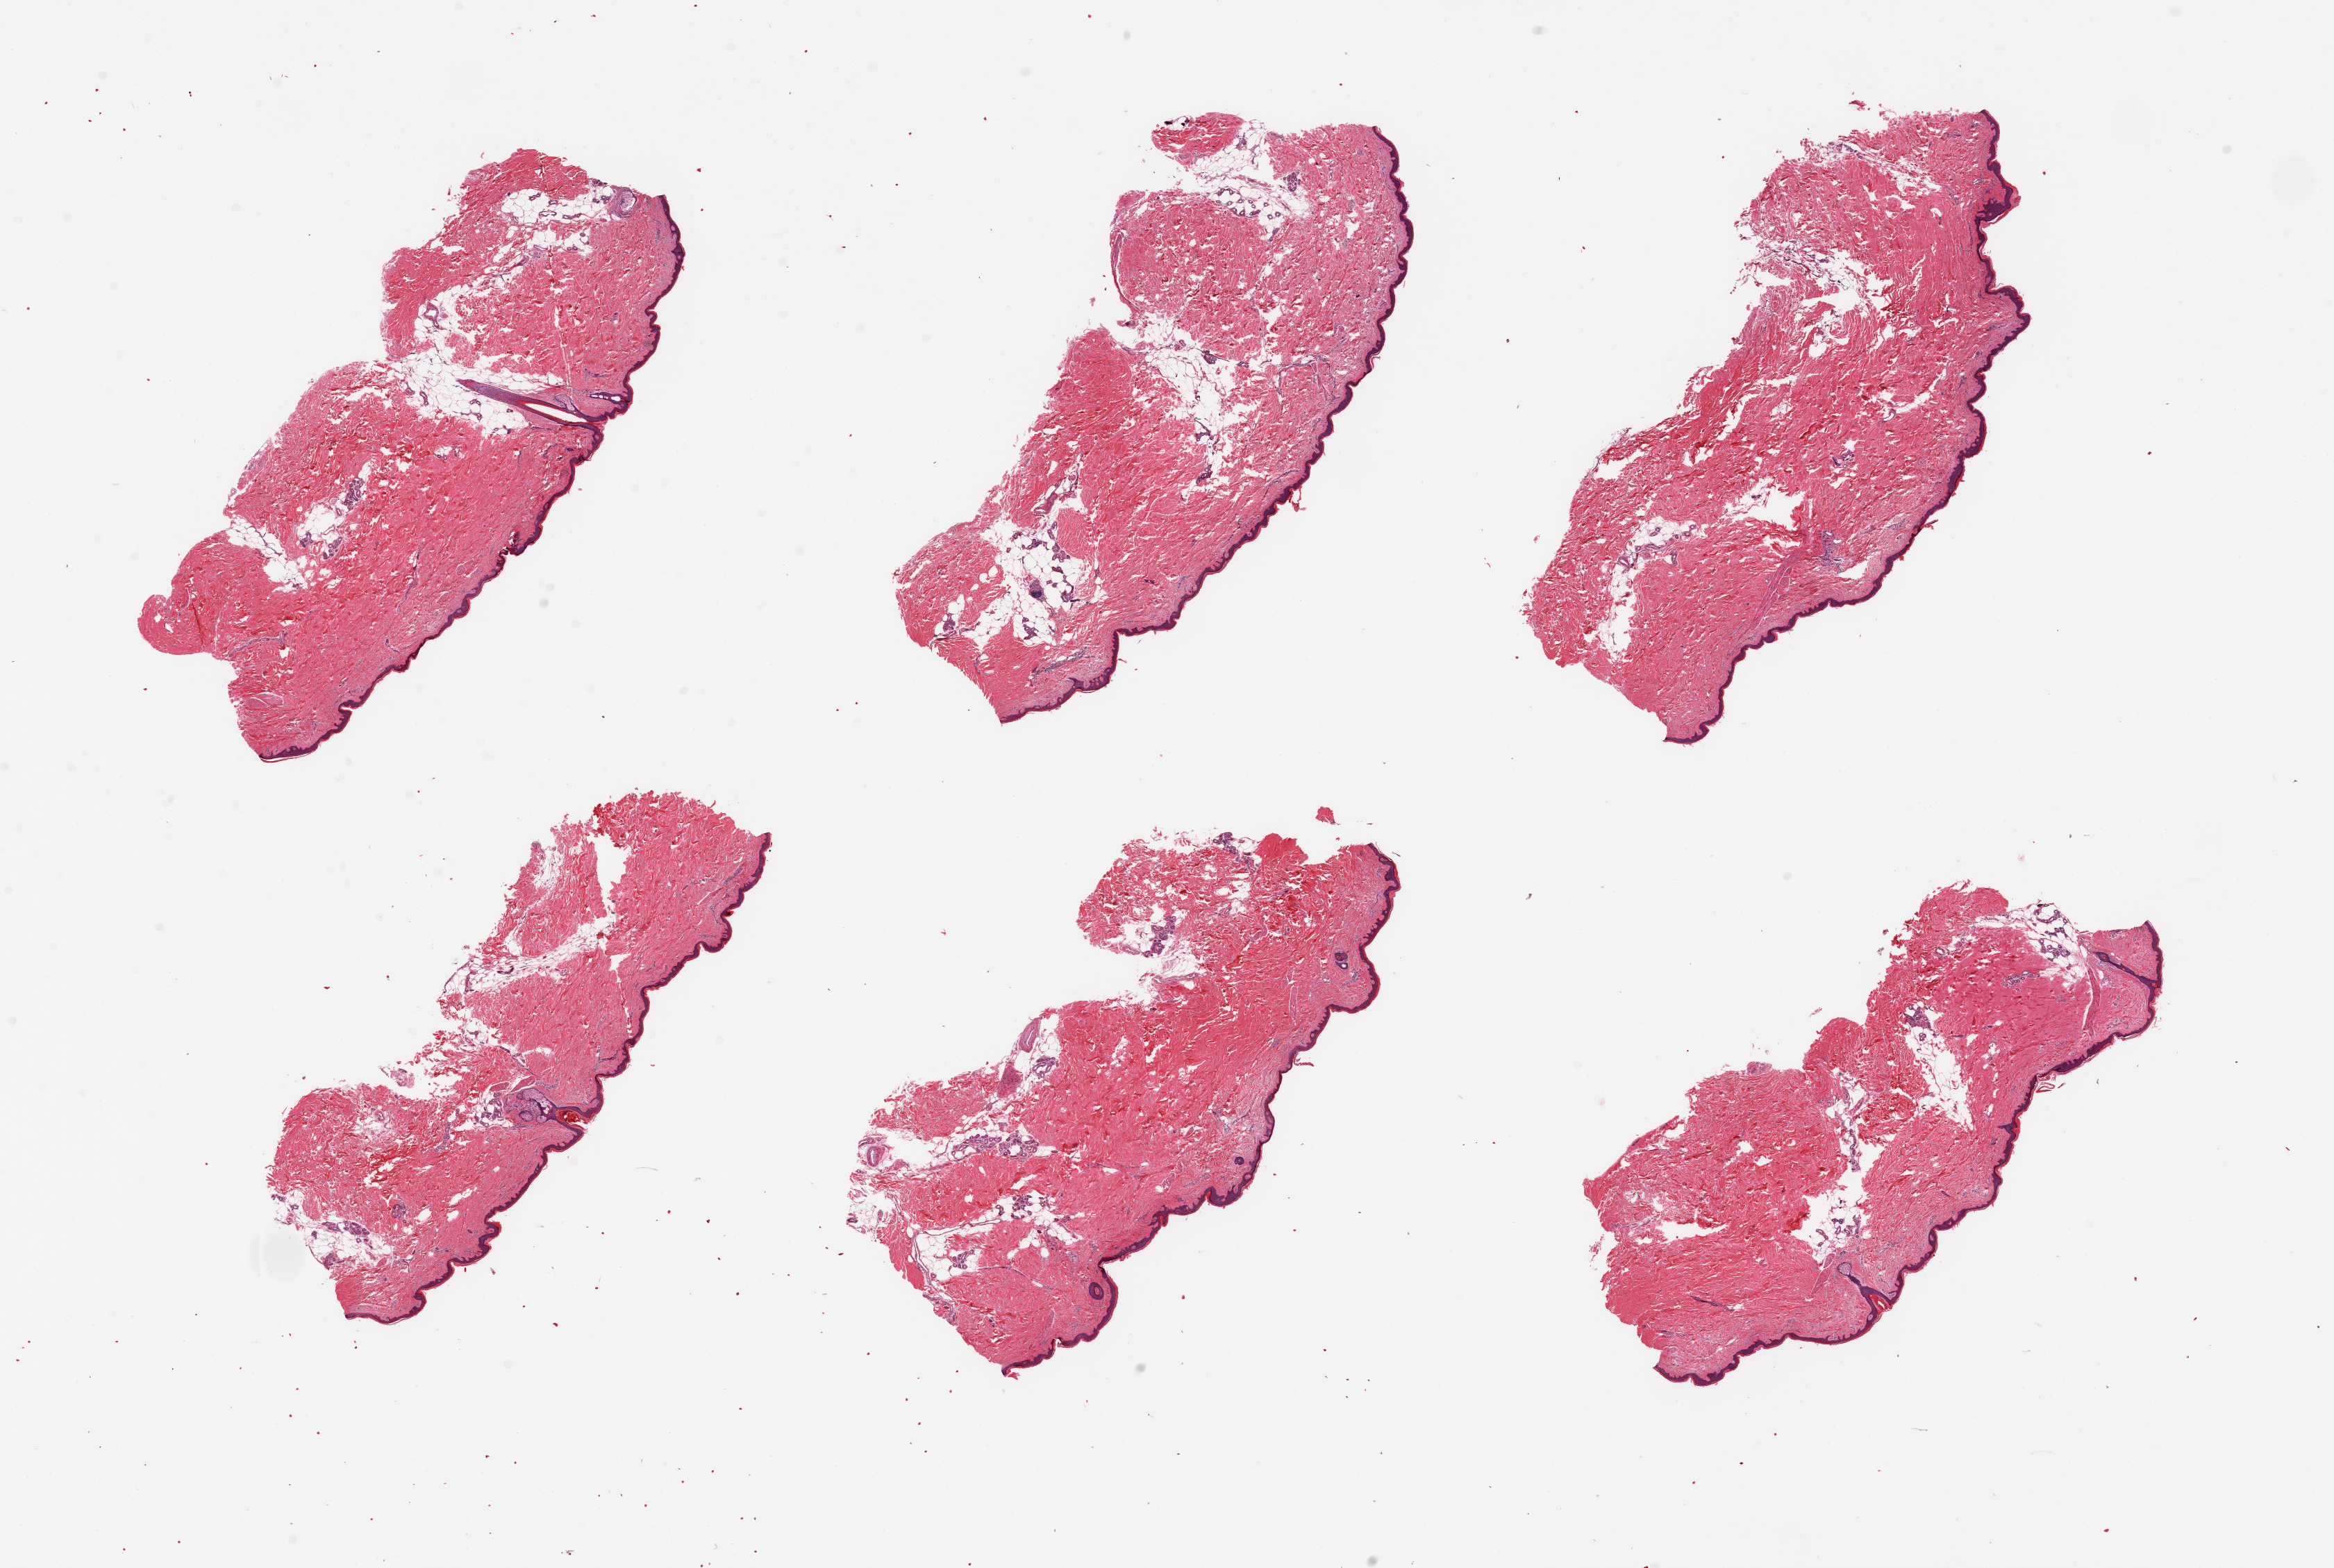
Digitized hematoxylin and eosin (H&E)-stained section, a low-resolution overview of the entire scanned area, about 26.6 x 17.9 mm; PAXgene-fixed, paraffin-embedded tissue; sampled site (target tissue): skin of lower leg; donor tissue sample. Donor: male.
Review note (as recorded): 6 pieces, trace dermal fat; squamous epithelium is ~40 microns.